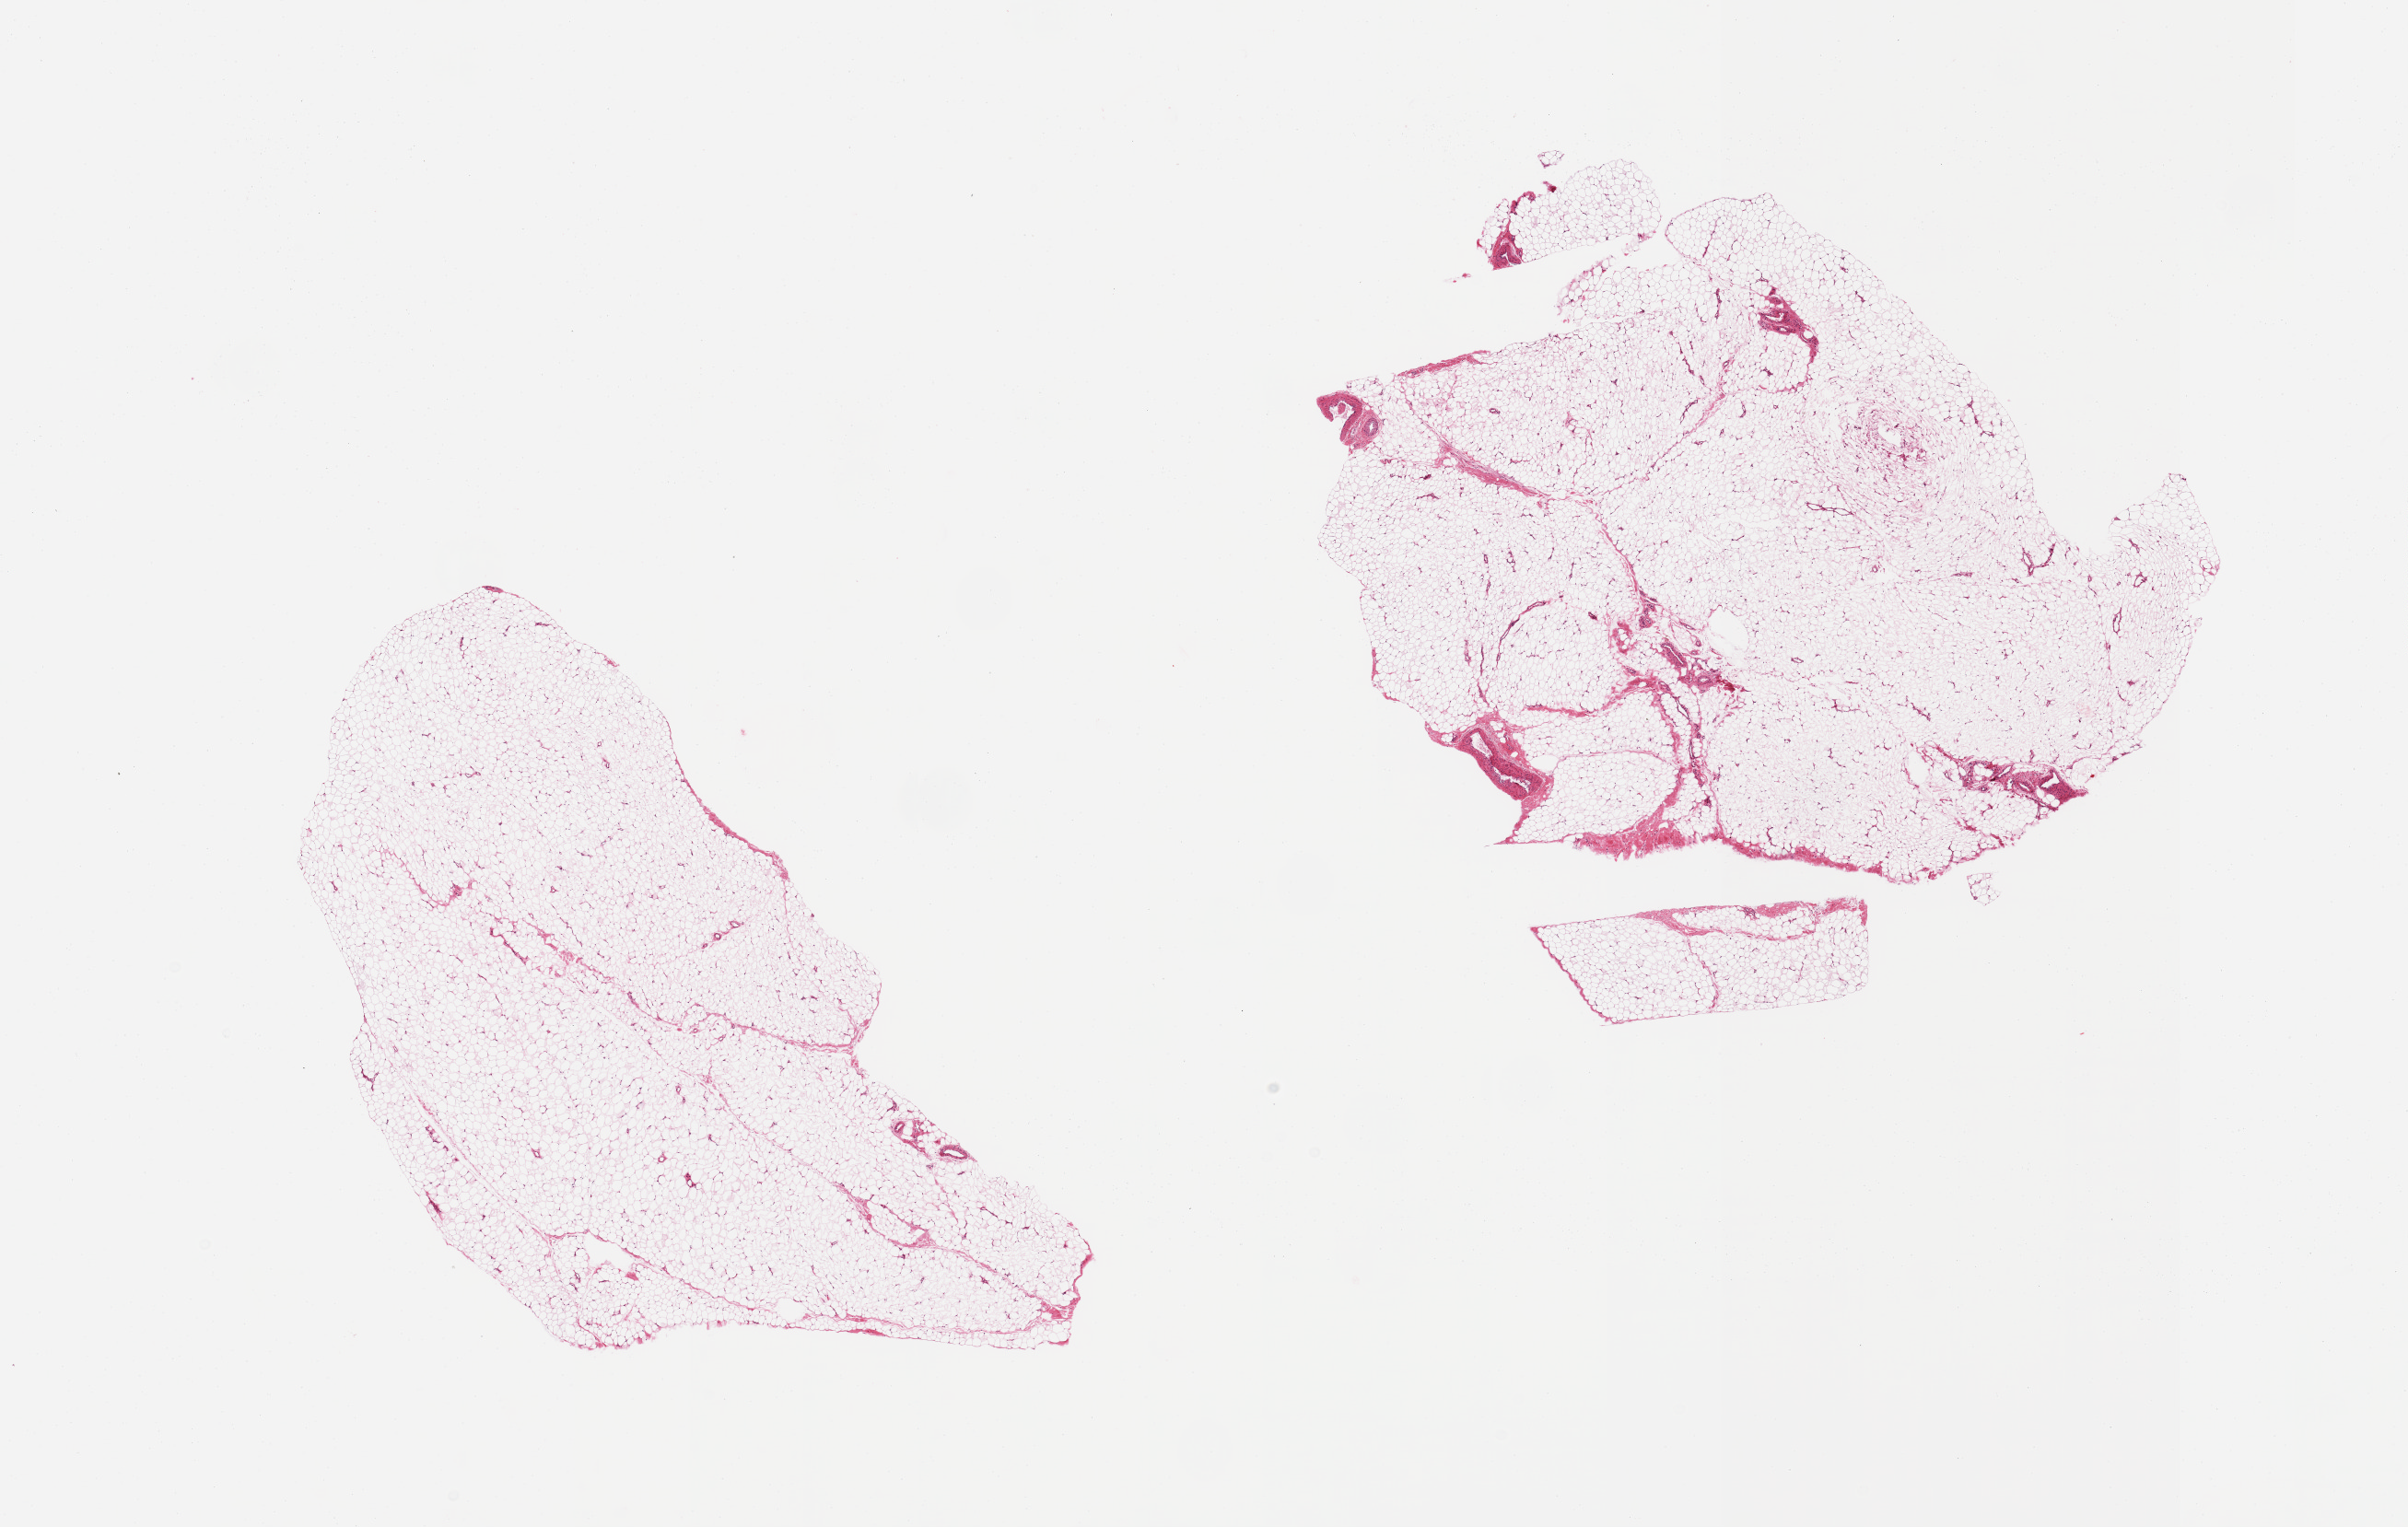
Whole-slide image, haematoxylin and eosin stain, low-resolution overview of the scanned area, about 20.7 x 13.1 mm (from a 20x scan); PAXgene-fixed, paraffin-embedded tissue; section of adipose tissue (target tissue); donor tissue sample.
Pathologist's review note for this sample: 2 pieces, ~5-10% fascia/vascular elements.